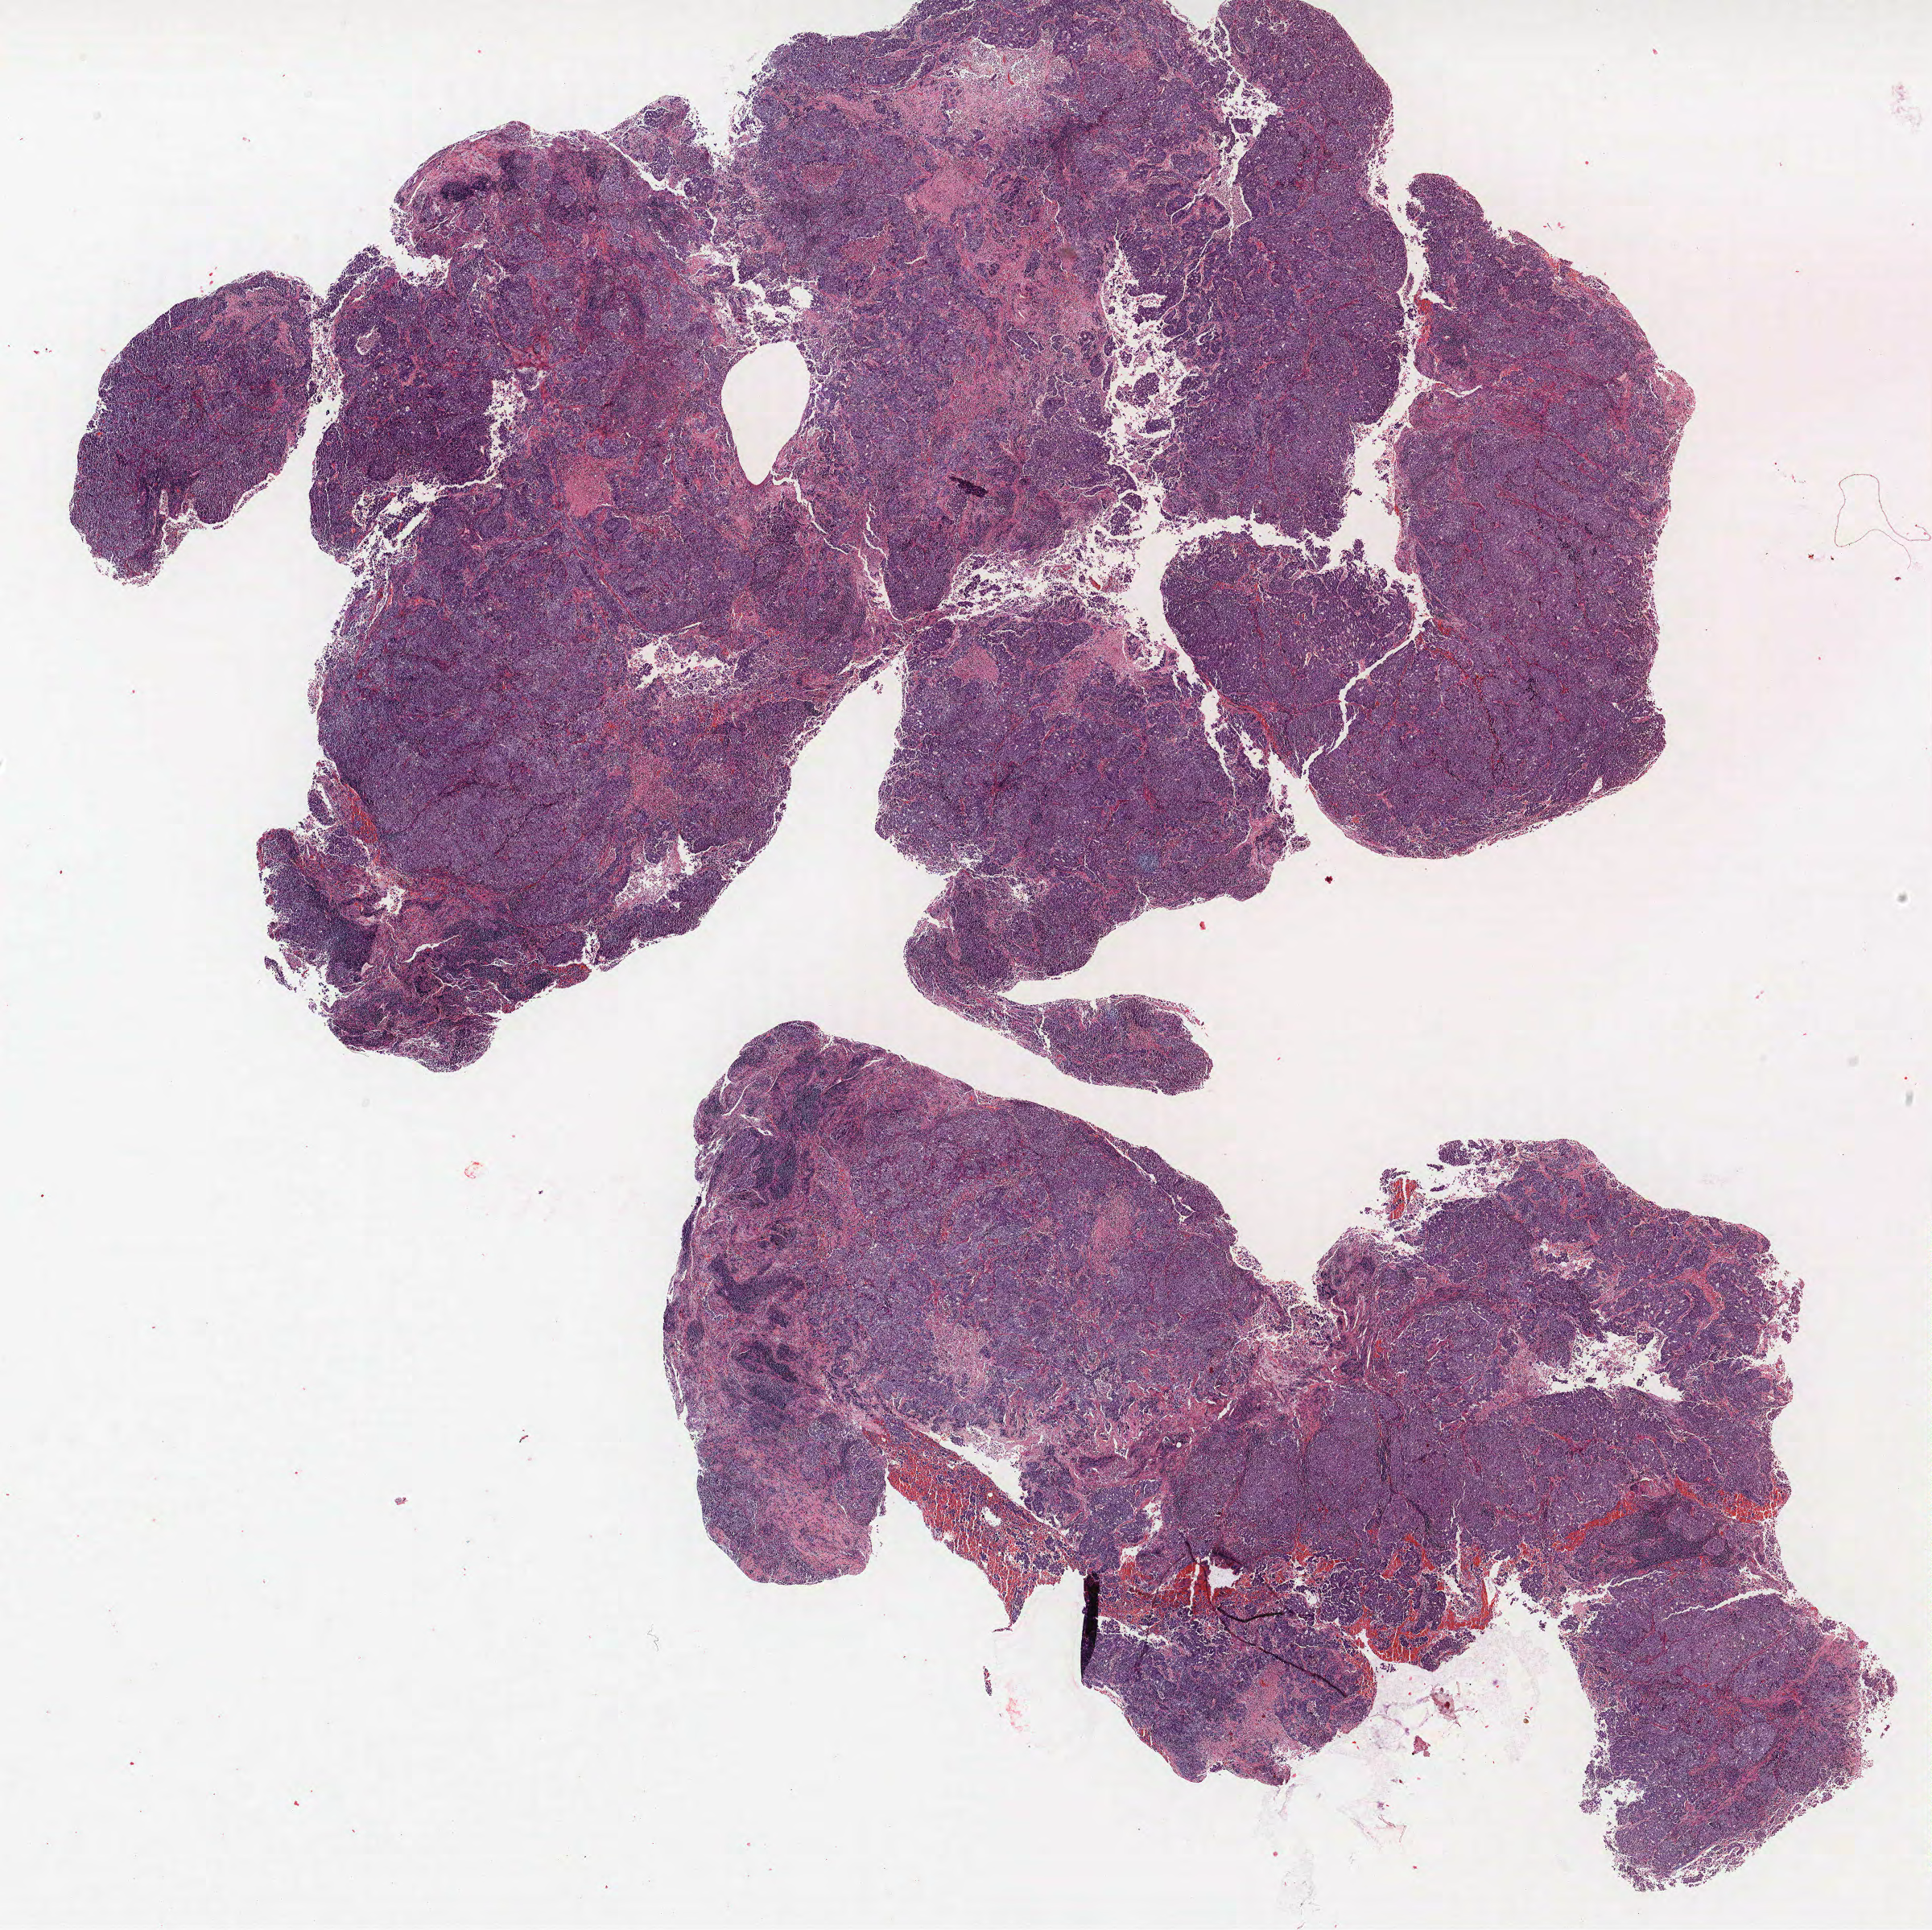
H&E whole-slide image, a low-resolution overview of the entire scanned area, about 19.2 x 19.2 mm (slide scanned at 40x); formalin-fixed paraffin-embedded (FFPE) section; lung tissue. Female, age 59 at enrolment. Current smoker at enrolment. Grade: cannot be assessed (GX).
- primary tumour location (clinical record): right lower lobe
- stage (AJCC 6th edition): IIIA
- participant's lung-cancer diagnosis: Adenocarcinoma, NOS
- tumour size (pathology): 31 mm